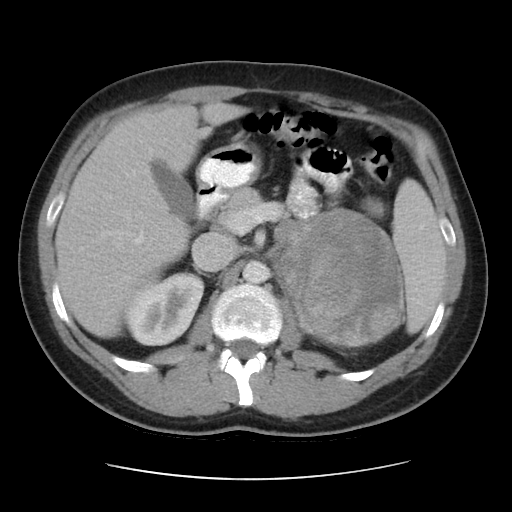
Contrast-enhanced abdominal CT, one axial slice; 120 kVp; intravenous contrast given; soft-tissue window (W 400 / L 40 HU); 512 × 512 image matrix. Male patient, age 32 years. From the clinical record (not read from this slice): diagnosis: adrenocortical carcinoma; tumour side: left adrenal; tumour size at pathology: 14 cm; Ki-67 index: 67 %; stage (as recorded): 3.
Structures marked on this image (semi-automatic segmentation, software-assisted and operator-edited):
- mass: bounding box <282,211,402,343> (left, top, right, bottom; pixels)